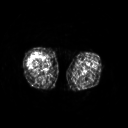
FDG PET of an extremity soft-tissue mass (from a PET/CT study), one axial slice. Slice 212 of 311 in the series (ordered by position). 3.27 mm slice thickness. 128 × 128 image matrix, field of view 500 × 500 mm. Patient: female, 57 years. Case-level facts recorded for this patient, not image findings: histological type: pleiomorphic undifferentiated sarcoma; grade: high; site of the primary tumour: right quadricep.
Annotated regions visible in this slice (expert contour drawn on MRI and transferred to this co-registered scan by the dataset authors):
- tumour plus oedema (research contour): box from (x=27, y=52) to (x=41, y=66) px